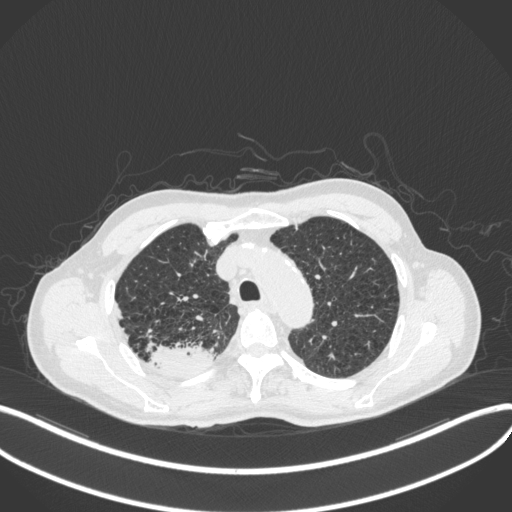
Chest CT, one axial slice; slice 340 of 423 in the series (ordered by position); reconstruction kernel B31f; 120 kVp; lung window (W 1500 / L -600 HU); 1 mm slice thickness; 512 × 512 image matrix, field of view 400 × 400 mm. Patient: male, 79 years. From the clinical record (not read from this slice): clinical TNM (as recorded): T3 N0 M0.
Annotated regions visible in this slice (rectangle marked by the reading radiologist):
- lung tumour (recorded histology: adenocarcinoma): bounding box <143,342,219,379> (left, top, right, bottom; pixels)